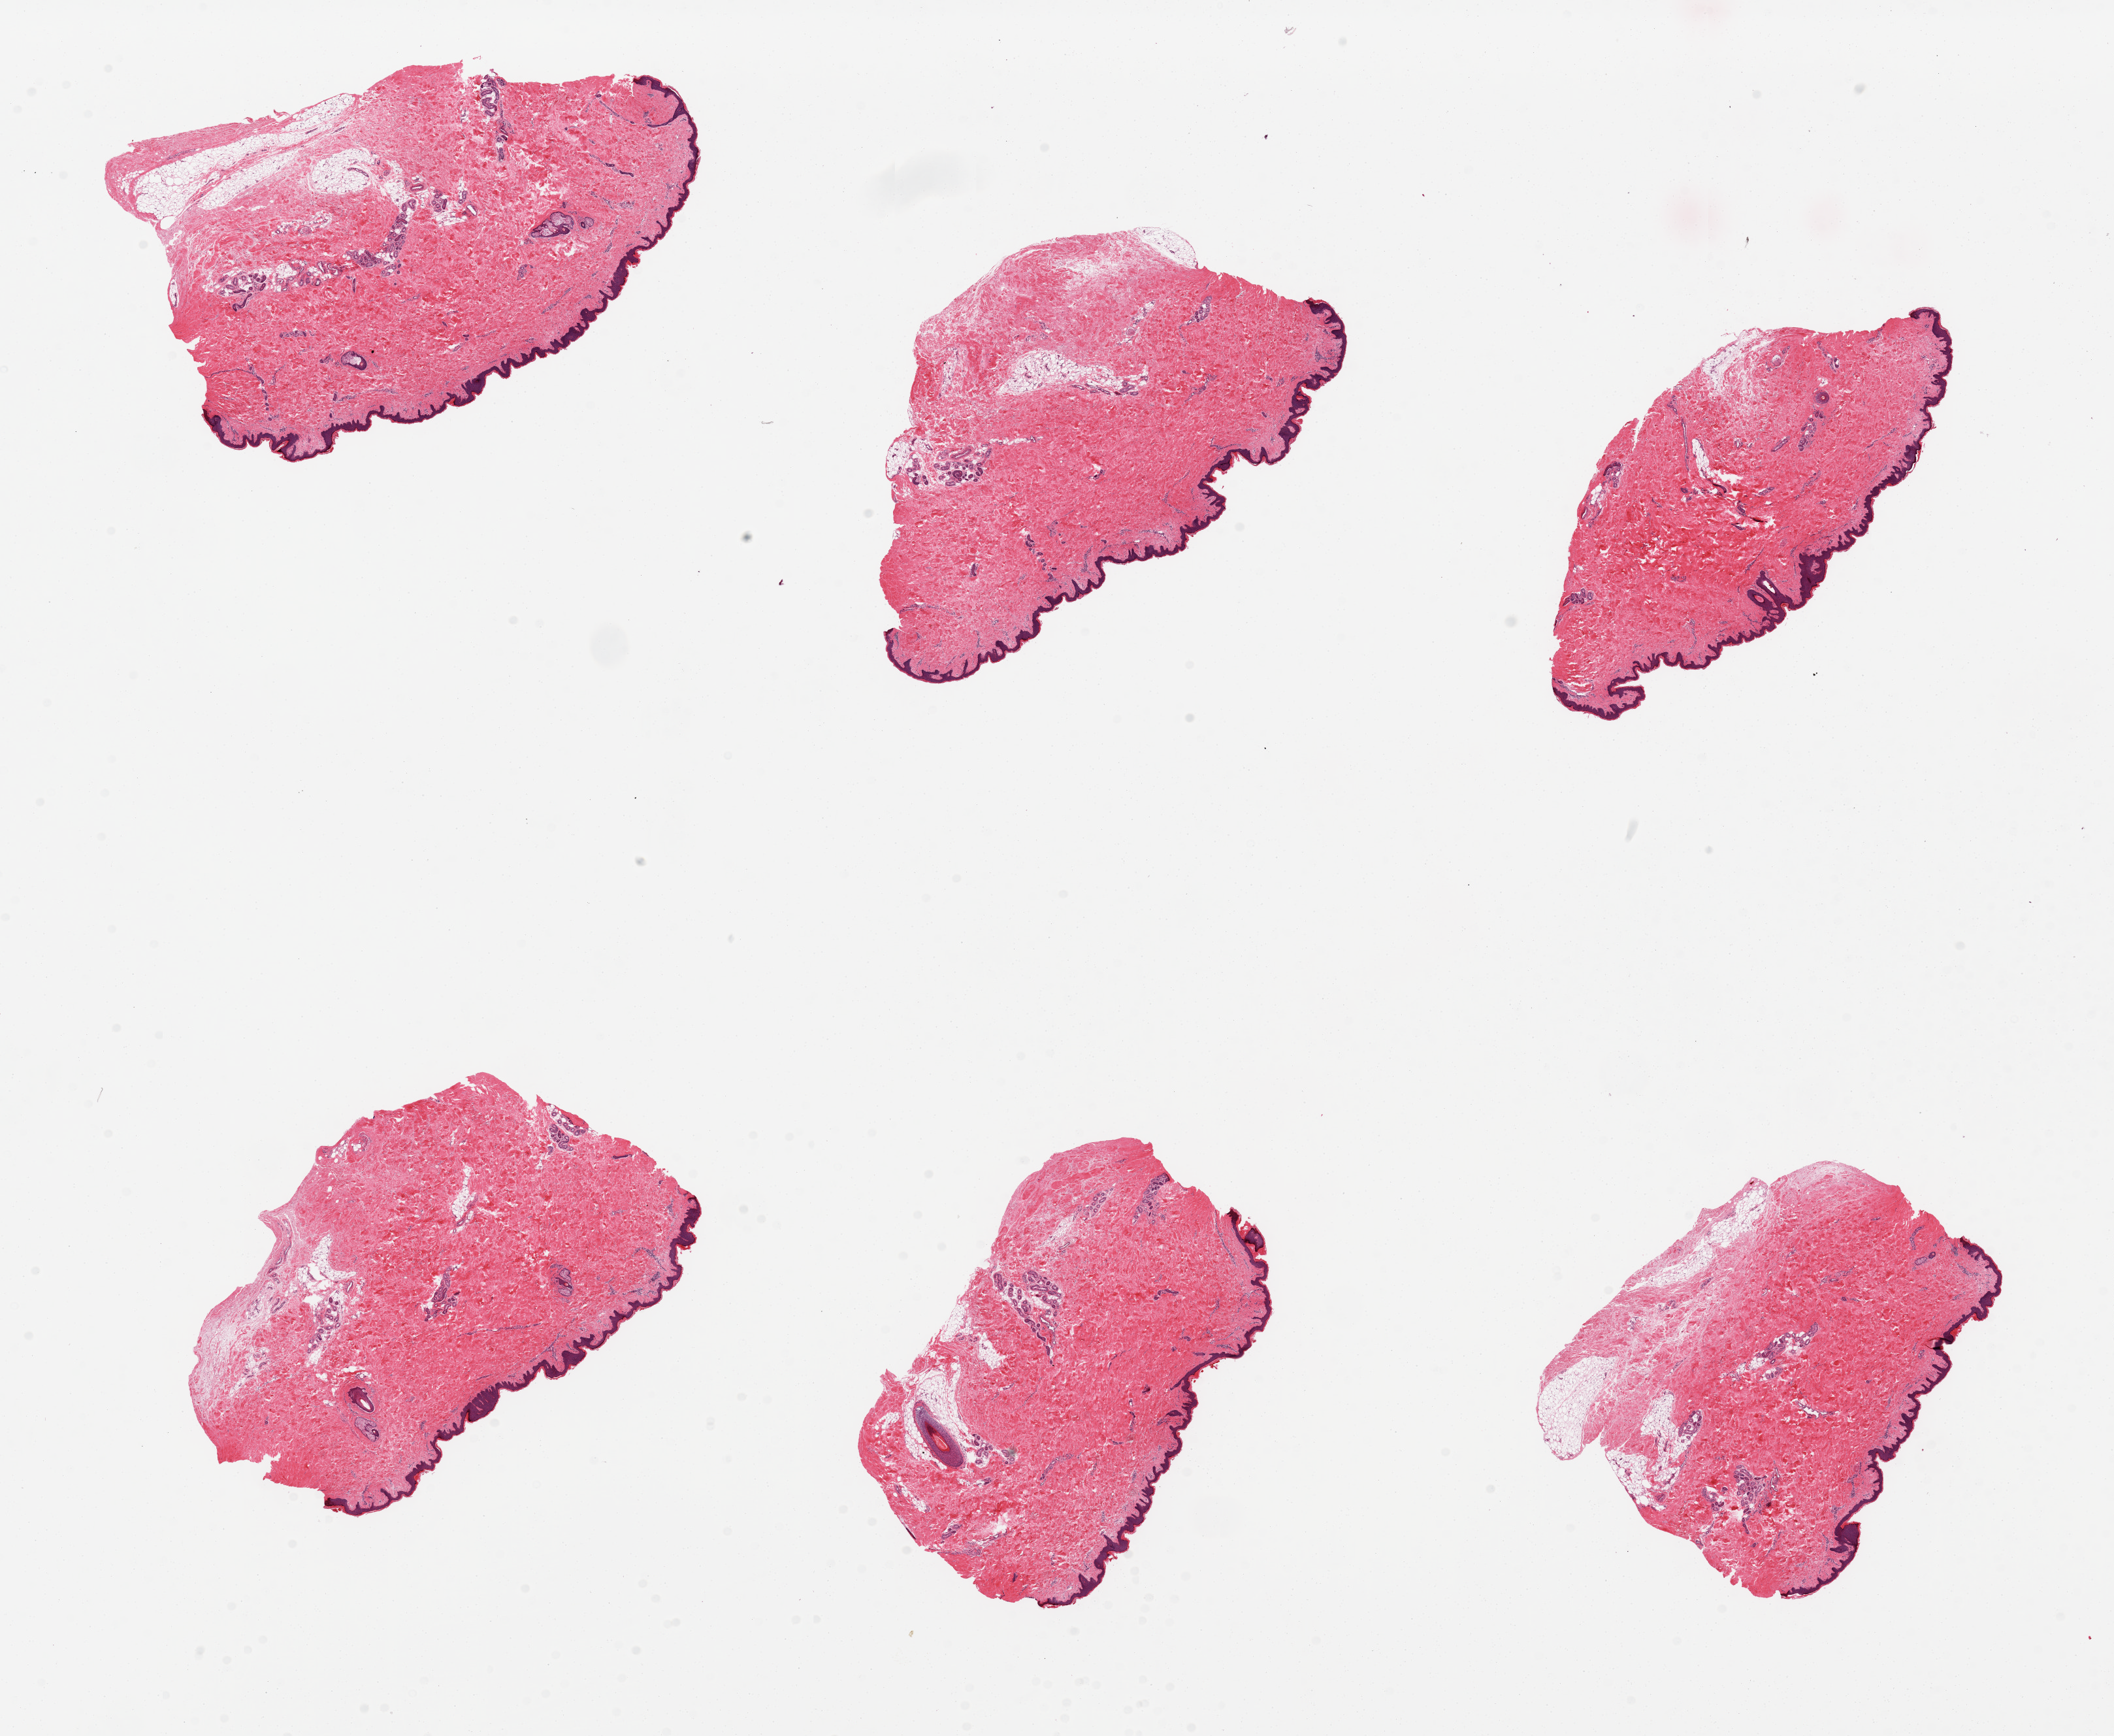
Digitized haematoxylin and eosin-stained section, brightfield, shown as a low-resolution overview of the whole scanned area (about 25.6 x 21.0 mm, slide scanned at 20x). PAXgene-fixed paraffin-embedded (PFPE) section. Section of skin of lower leg (target tissue). Tissue donor sample. Male donor.
* review note (as recorded): 6 pieces